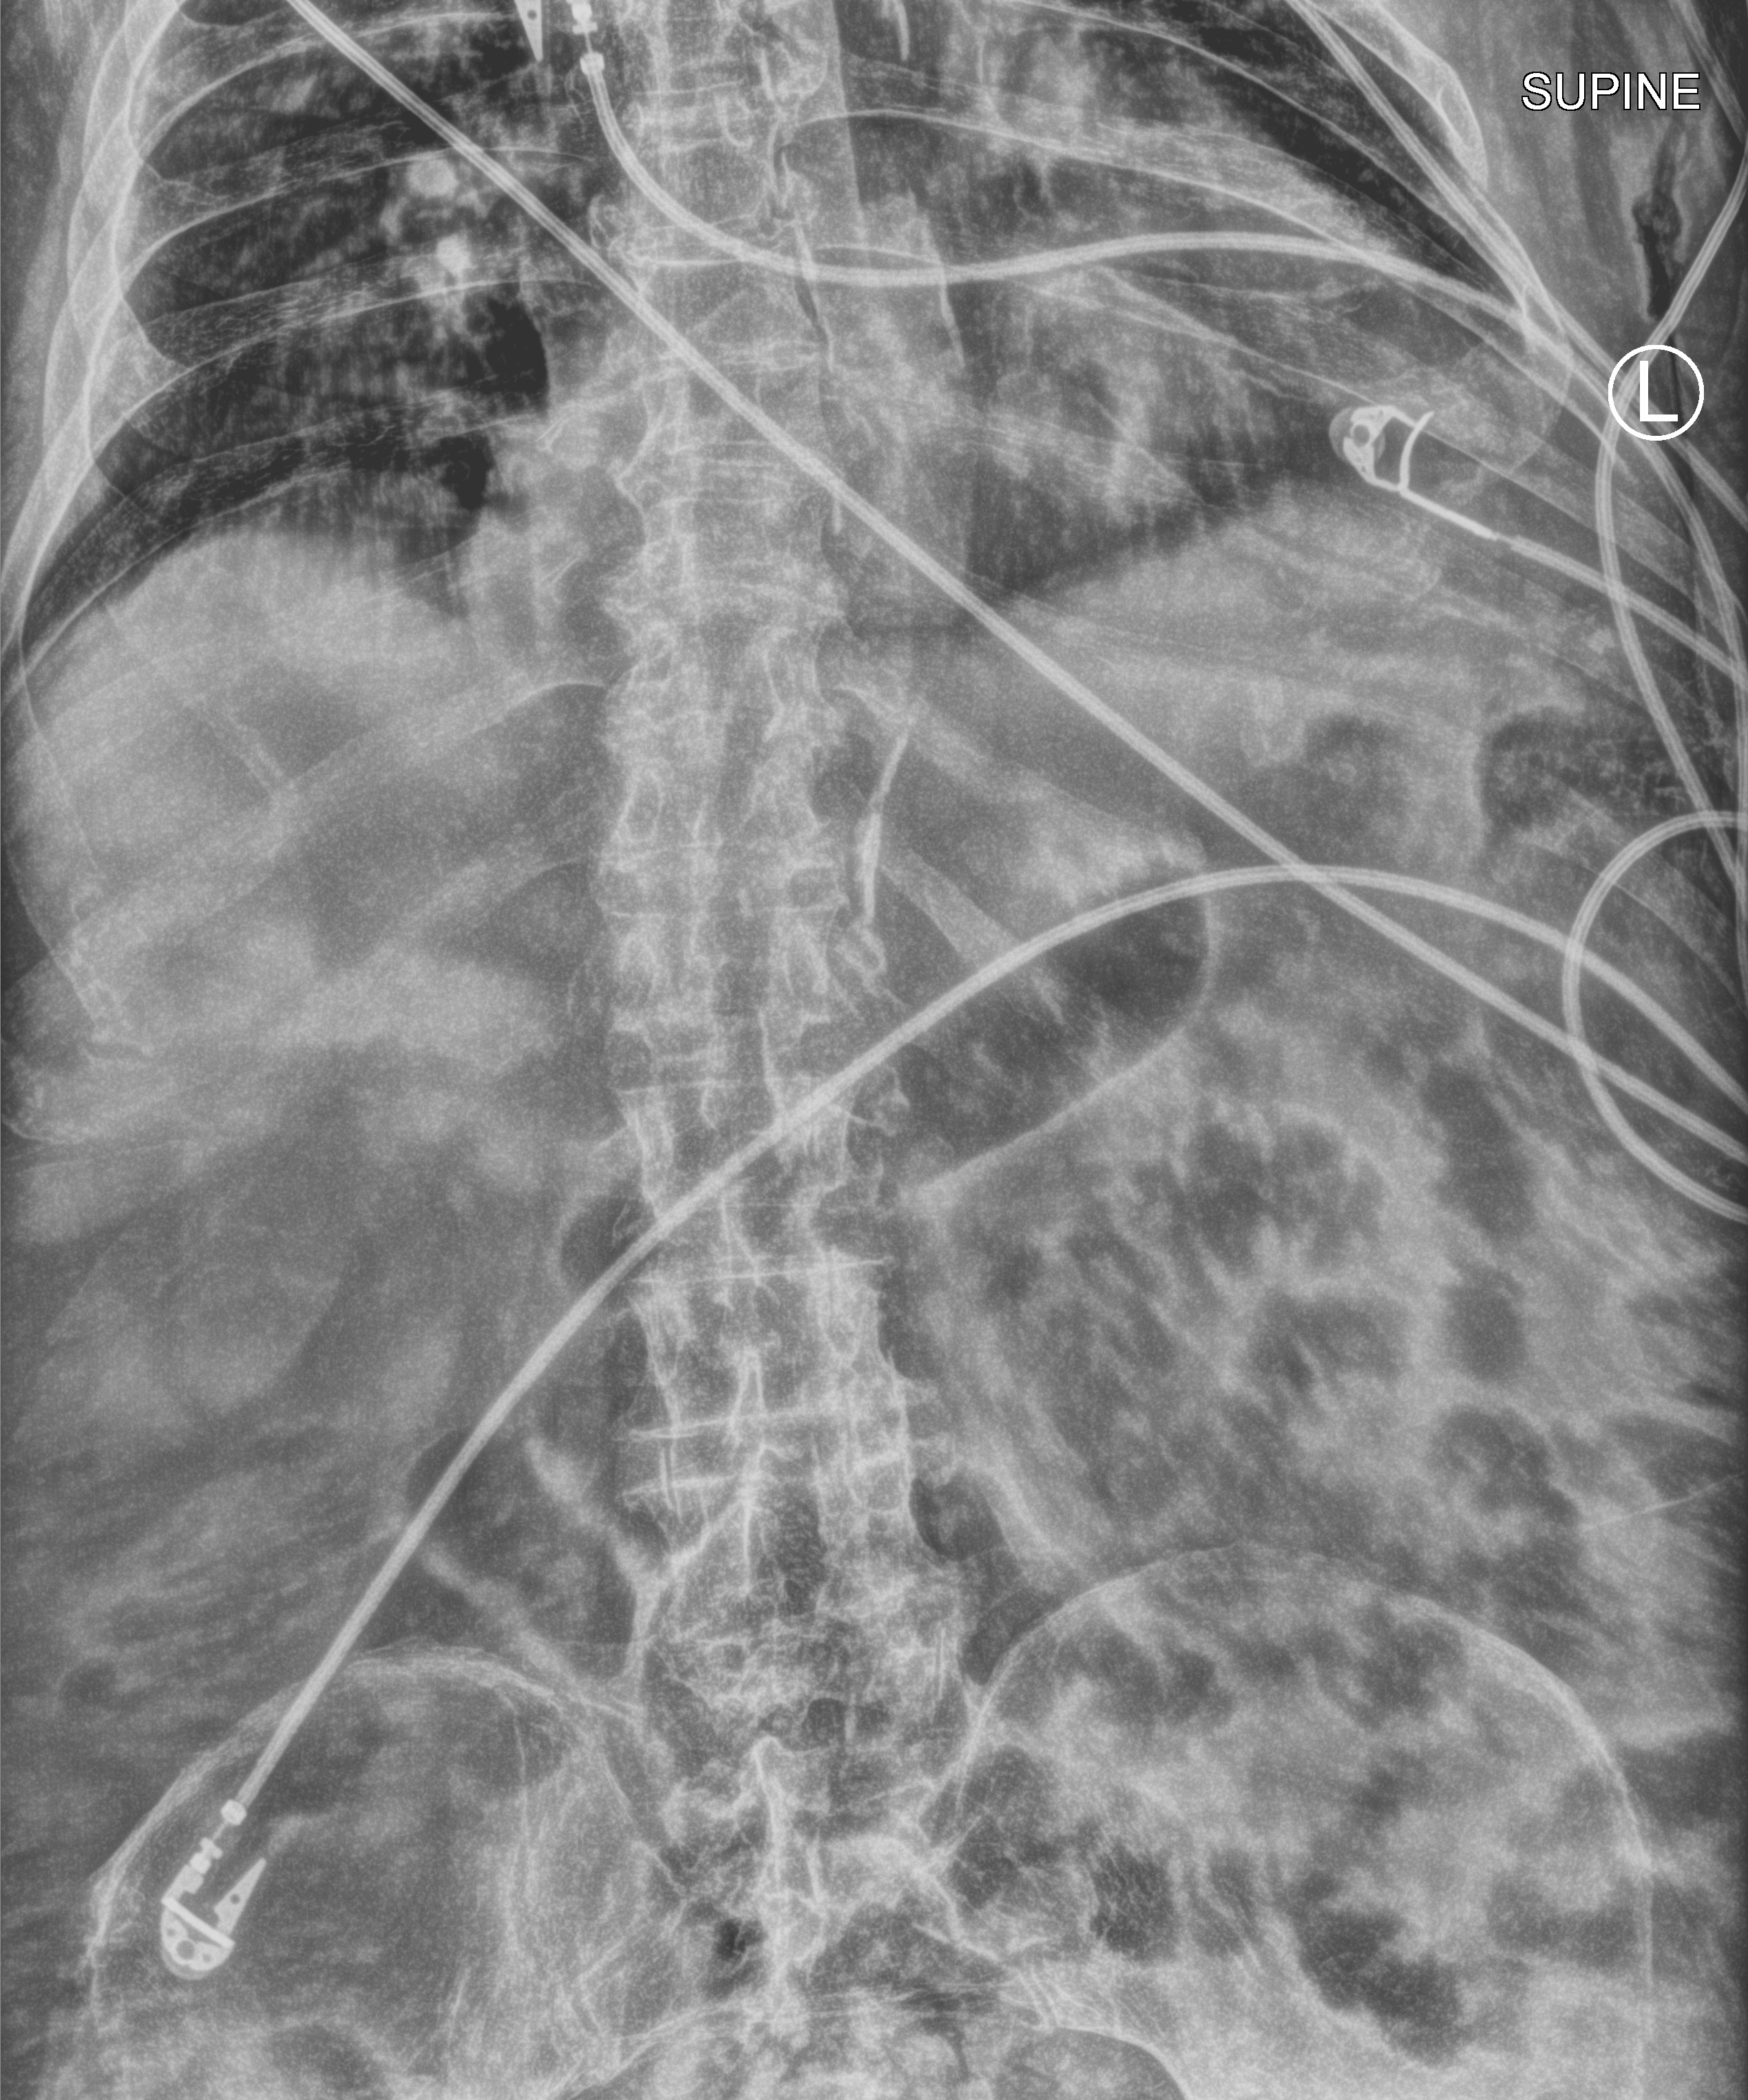
Abdomen X-ray (portable). Patient hospitalised with COVID-19; male, aged 75–90 years.
Admission-level facts for this patient (not findings on this image; timing relative to this image not recorded): admitted to intensive care during this hospital stay: no.